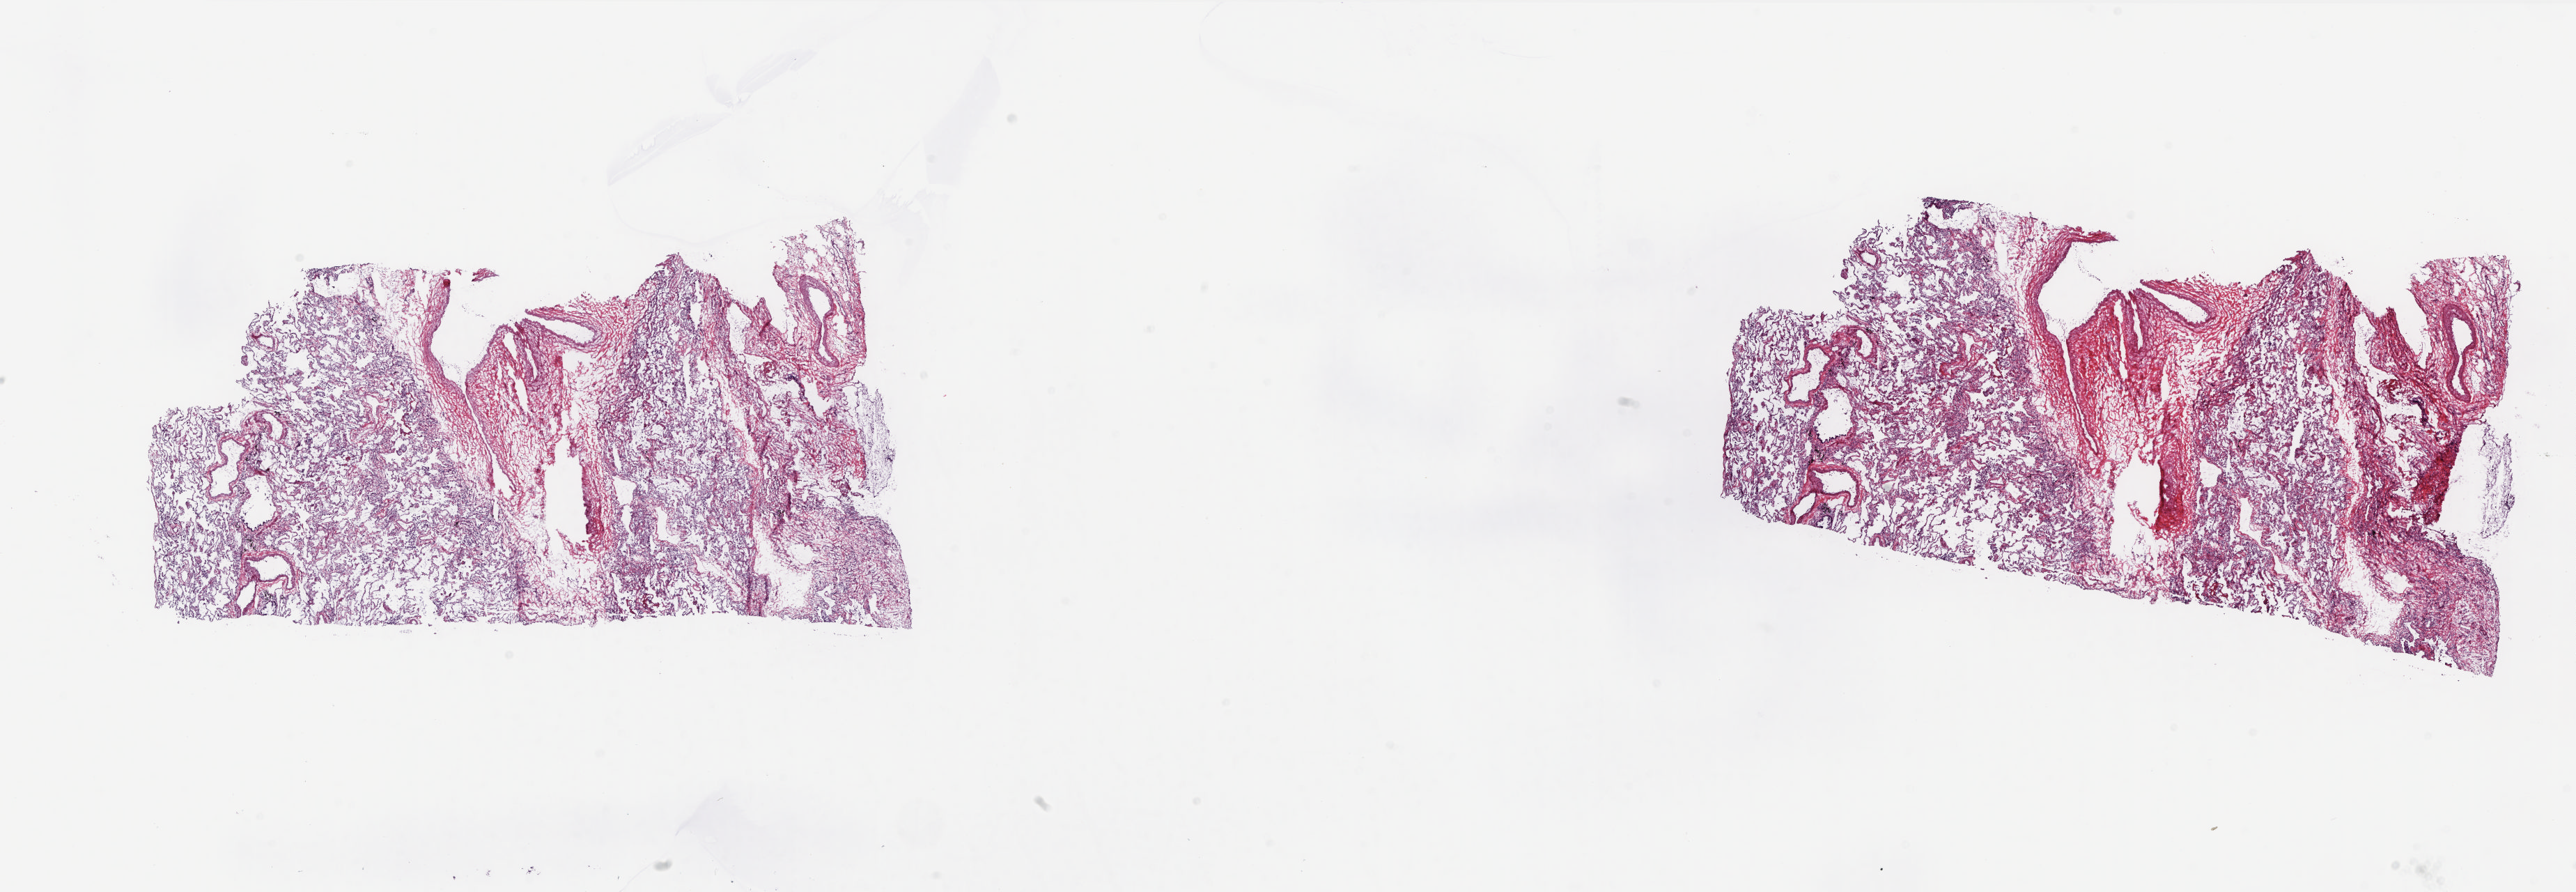
H&E whole-slide image — a low-resolution overview of the entire scanned area, about 29.8 x 10.3 mm (acquisition: 20x scan), frozen section from the top of the tissue portion, sample: solid tissue normal (non-tumour tissue), lung. Female patient; age at initial diagnosis 60 years. Composition of this section per pathologist review: tumour cells 0%, tumour nuclei 0%, normal cells 100%, stromal cells 0%, necrosis 0%. Infiltration values recorded for this section: lymphocyte infiltration 20%, monocyte infiltration 20%, neutrophil infiltration 40%.
This section: solid tissue normal (non-tumour) sample from the same patient. Patient diagnosis: Adenocarcinoma, NOS (upper lobe, lung).